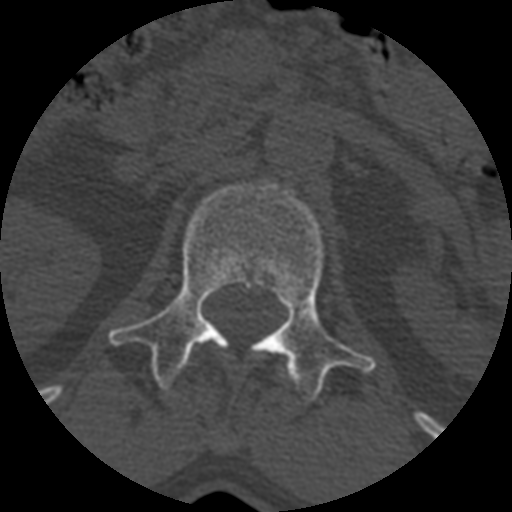
CT including the spine, one axial slice. Position 363 of 399 along the scan axis. Reconstruction kernel STANDARD. 120 kVp. Bone window (W 1800 / L 400 HU). 1.25 mm slice thickness. 512 × 512 image matrix. Patient age 71 years. Case-level facts recorded for this patient, not image findings: primary cancer: prostate.
Outlined on this slice (semi-automatic segmentation, software-assisted and operator-edited):
- L1 vertebra: bounding box <110,178,374,405> (left, top, right, bottom; pixels)